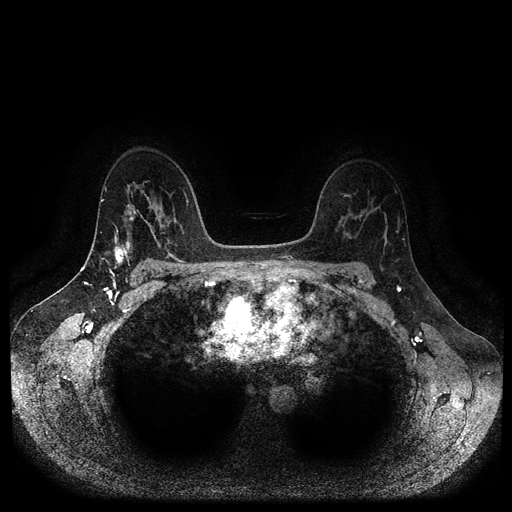
Breast MRI (dynamic contrast-enhanced, multi-phase), one axial slice; position 69 of 116 along the scan axis; dynamic contrast-enhanced series, time point 2 of 5 at this slice position (early post-contrast); 1.5 T; TE 2.6 ms, TR 5.3 ms; 2 mm slice thickness; 512 × 512 image matrix. Female patient, age 45 years.
Annotated regions visible in this slice (semi-automatically segmented with operator editing):
- breast lesion (labelled 'tumour' in the annotation; benign lesions carry a separate 'benign' label): bounding box (x1, y1, x2, y2) in pixels: (112, 242, 132, 270)